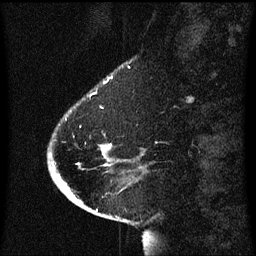
Breast MRI (dynamic contrast-enhanced), one sagittal slice. Position 14 of 60 along the scan axis. Dynamic contrast-enhanced series, image 2 of 3 at this slice position (ordered by acquisition). 1.5 T. TE 4.2 ms, TR 8.4 ms. 256 × 256 image matrix, field of view 200 × 200 mm. Female patient, age 54 years. From the clinical record (not read from this slice): setting: breast cancer imaged before/during neoadjuvant chemotherapy; receptor status: HR-positive, HER2-negative.
Structures marked on this image (semi-automatically segmented with operator editing):
- analysis volume of interest (the breast-tissue region the enhancement analysis was run in; not a lesion): bounding box <48,108,119,171> (left, top, right, bottom; pixels)
- tumour enhancement mask (voxels above the 70 % enhancement threshold inside the analysis volume of interest): <102,146,112,153>